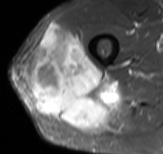
MRI of an extremity soft-tissue mass, one axial slice. Position 47 of 61 along the scan axis. STIR. MR volume resampled by the dataset authors to the PET/CT grid (not the native acquisition matrix). 3.27 mm slice thickness. 163 × 154 image matrix, field of view 159 × 150 mm. Male patient. Case-level facts recorded for this patient, not image findings: histological type: poorly differentiated synovial sarcoma; grade: high; site of the primary tumour: right buttock.
Outlined on this slice (expert contour drawn on MRI and transferred to this co-registered scan by the dataset authors):
- gross tumour volume including surrounding oedema: bounding box (x1, y1, x2, y2) in pixels: (27, 25, 120, 127)
- gross tumour volume (mass): (27, 25, 120, 127)